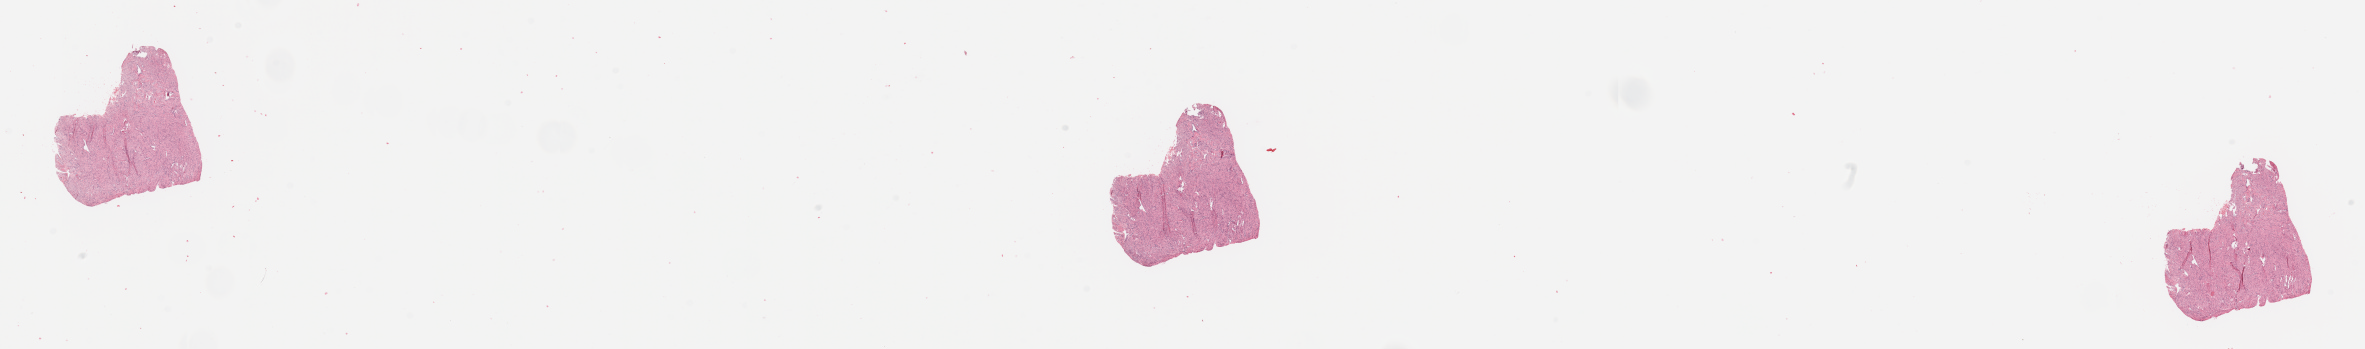
Whole-slide histology image, H&E — whole scanned area (about 37.4 x 5.5 mm, from a 20x scan) shown as a low-resolution overview. Uterus, normal (non-tumour) tissue. Patient: female, age 53 years.
• this section: normal (non-tumour) tissue from the same patient
• patient diagnosis: Endometrioid adenocarcinoma, NOS